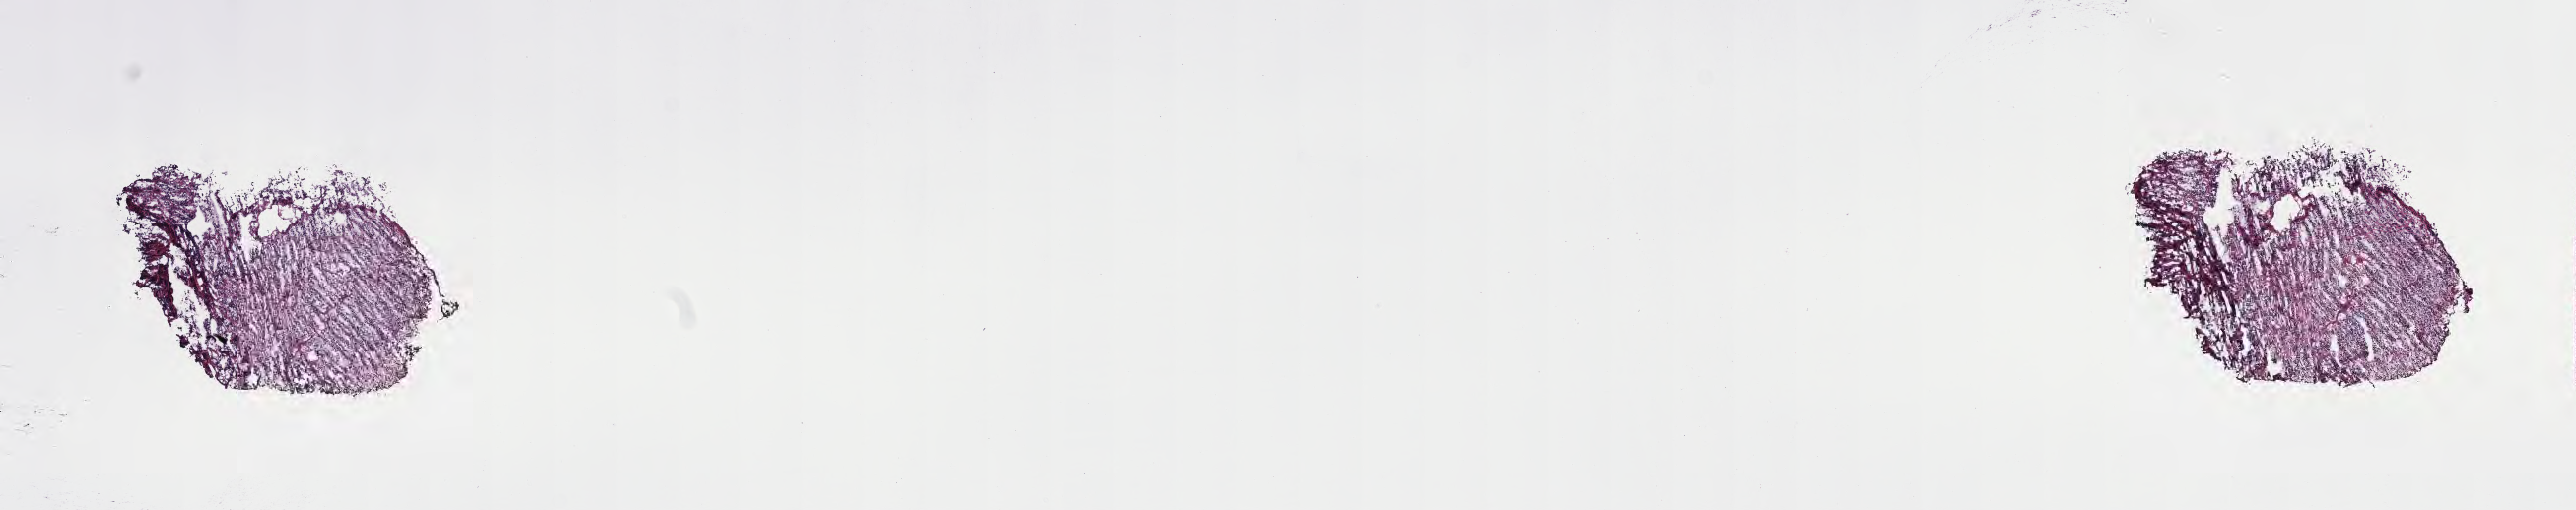
Digitized H&E-stained section of tumor tissue from the brain stem — a low-resolution overview of the entire scanned area, about 21.1 x 4.2 mm. Frozen section. Patient: male, age 51 months (4 years 3 months).
Diagnosis (ICD-O-3 morphology term): Medulloblastoma, NOS.